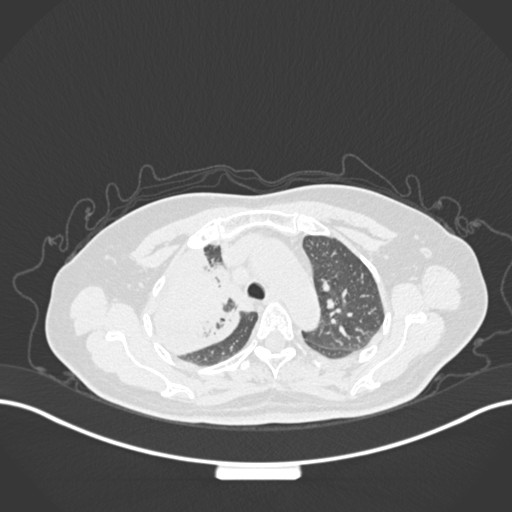
Chest CT, one axial slice. Slice 117 of 177 in the series (ordered by position). Reconstruction kernel B30f. 120 kVp. Lung window (W 1500 / L -600 HU). 1 mm slice thickness. 512 × 512 image matrix, field of view 400 × 400 mm. Patient: female, 60 years. From the clinical record (not read from this slice): clinical TNM (as recorded): T3 N1 M1.
Structures marked on this image (bounding box drawn by a radiologist):
- lung tumour (recorded histology: adenocarcinoma): box from (x=148, y=246) to (x=244, y=366) px